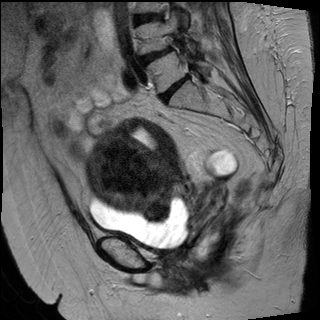
Pelvic MRI for cervical cancer, one sagittal slice; slice 28 of 50 in the series (ordered by position); T2-weighted; 1.5 T; TE 89 ms, TR 4880 ms; 320 × 320 image matrix, field of view 260 × 260 mm. Female patient, age 50 years.
Outlined on this slice (outlined manually by an expert reader):
- uterus and cervix: bounding box [x1, y1, x2, y2] px = [87, 117, 189, 221]